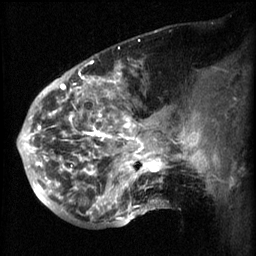
Breast MRI (dynamic contrast-enhanced), one sagittal slice. Slice 23 of 60 in the series (ordered by position). 3 images stored at this slice position (order not interpretable as contrast timing). 1.5 T. TE 4.2 ms, TR 8.2 ms. 256 × 256 image matrix, field of view 200 × 200 mm. Female patient, age 50 years.
Outlined on this slice (semi-automatic segmentation, software-assisted and operator-edited):
- analysis volume of interest (the breast-tissue region the enhancement analysis was run in; not a lesion): bounding box [x1, y1, x2, y2] px = [50, 64, 169, 217]
- tumour enhancement mask (voxels above the 70 % enhancement threshold inside the analysis volume of interest): [50, 64, 167, 215]